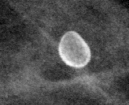
Cropped region of a digitized screen-film mammogram centred on a radiologist-marked abnormality; left breast; CC view; BI-RADS breast density category 2 (scale 1–4).
Calcifications, morphology lucent center; BI-RADS assessment category 2; benign without callback (not worked up further).